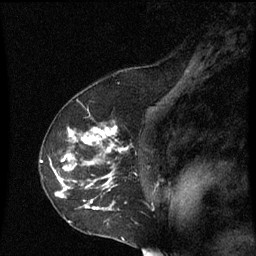
Breast MRI (dynamic contrast-enhanced), one sagittal slice. Position 43 of 60 along the scan axis. Dynamic contrast-enhanced series, image 2 of 3 at this slice position (ordered by acquisition). 1.5 T. TE 4.2 ms, TR 8.9 ms. 2 mm slice thickness. 256 × 256 image matrix, field of view 200 × 200 mm. Patient: female, 53 years. From the clinical record (not read from this slice): setting: breast cancer imaged before/during neoadjuvant chemotherapy; receptor status: HR-positive, HER2-negative.
Annotated regions visible in this slice (semi-automatically segmented with operator editing):
- analysis volume of interest (the breast-tissue region the enhancement analysis was run in; not a lesion): bounding box (x1, y1, x2, y2) in pixels: (40, 128, 131, 223)
- tumour enhancement mask (voxels above the 70 % enhancement threshold inside the analysis volume of interest): (54, 128, 125, 209)